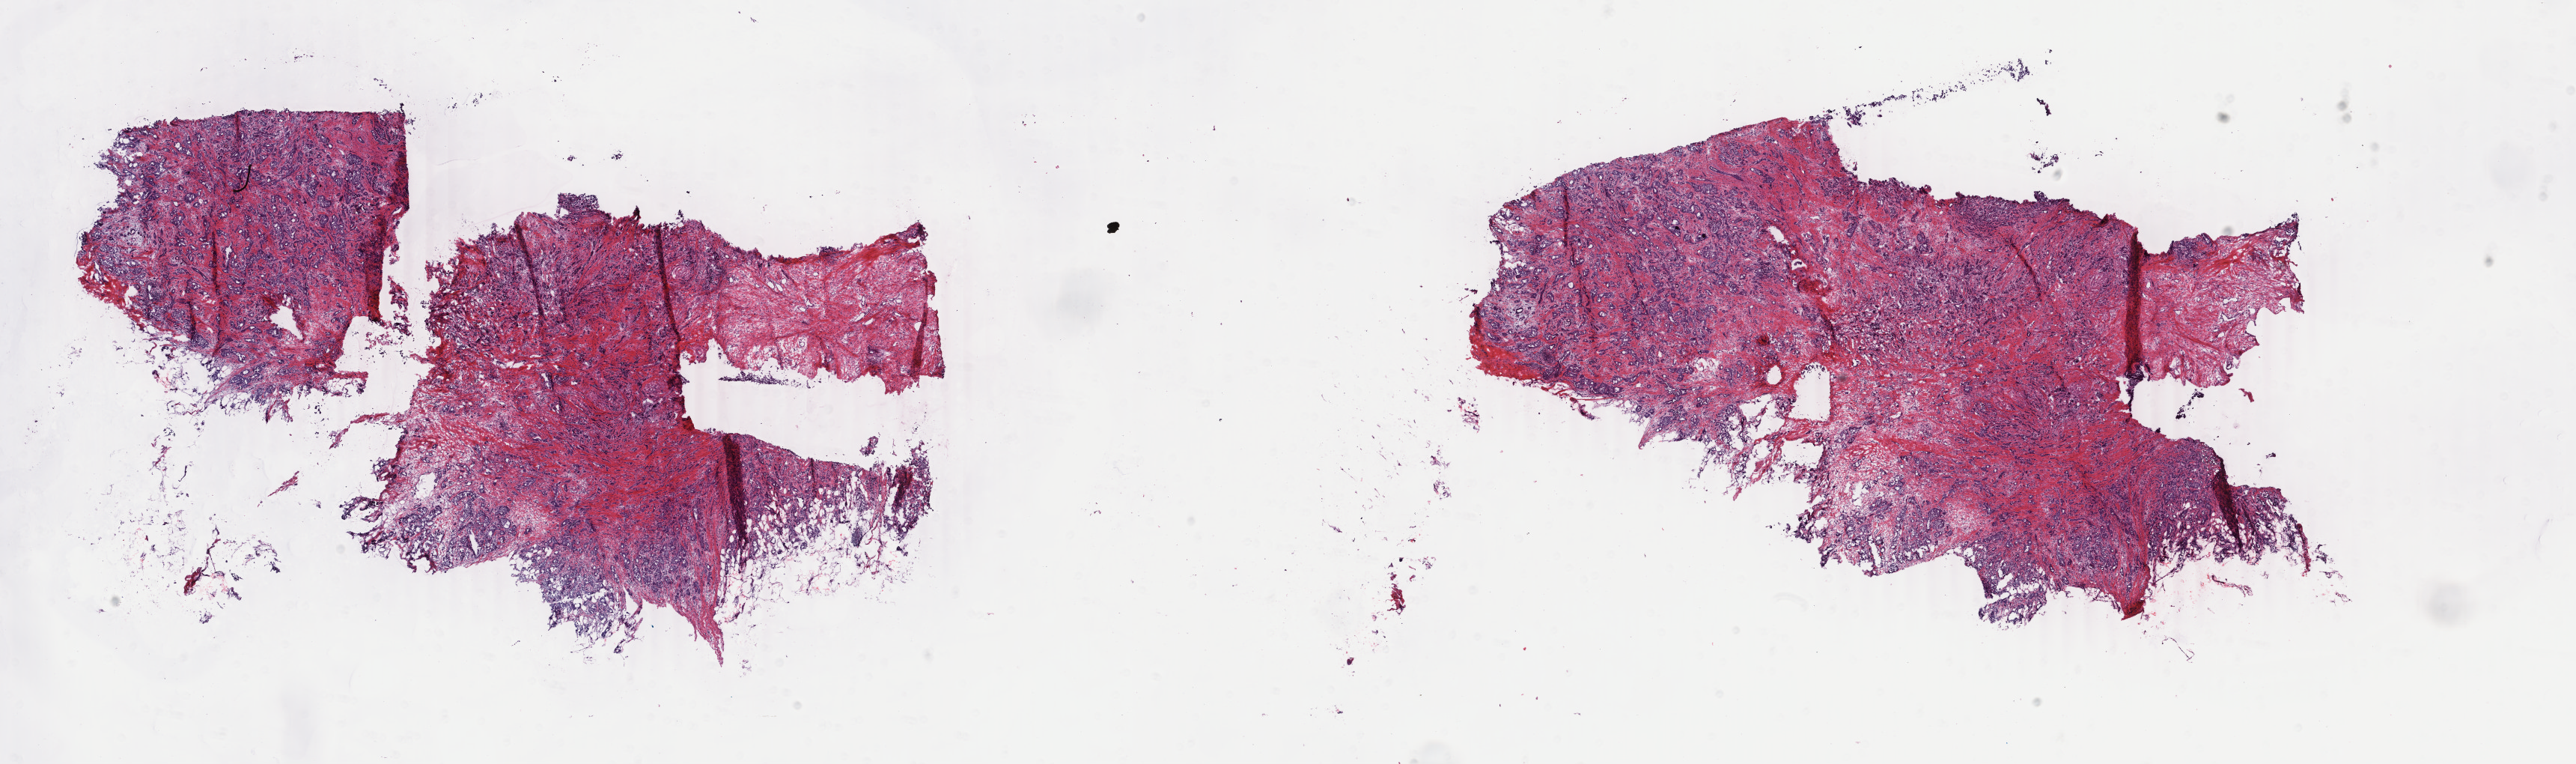
Digitized H&E-stained tissue section (whole slide) — whole scanned area (about 27.4 x 8.1 mm, slide scanned at 40x) shown as a low-resolution overview. Frozen section. Primary tumour sample from the breast. Patient: female, age at initial diagnosis 68 years. Slide review estimates, as recorded: tumour cells 85%, tumour nuclei 85%, normal cells 1%, stromal cells 14%, necrosis 0%. Infiltration values recorded for this section: lymphocyte infiltration 1%, monocyte infiltration 0%, neutrophil infiltration 0%.
Lymph nodes positive (case pathology): 2 of 14 examined. Histologic diagnosis: Infiltrating duct carcinoma, NOS. AJCC pathologic stage: IIA.